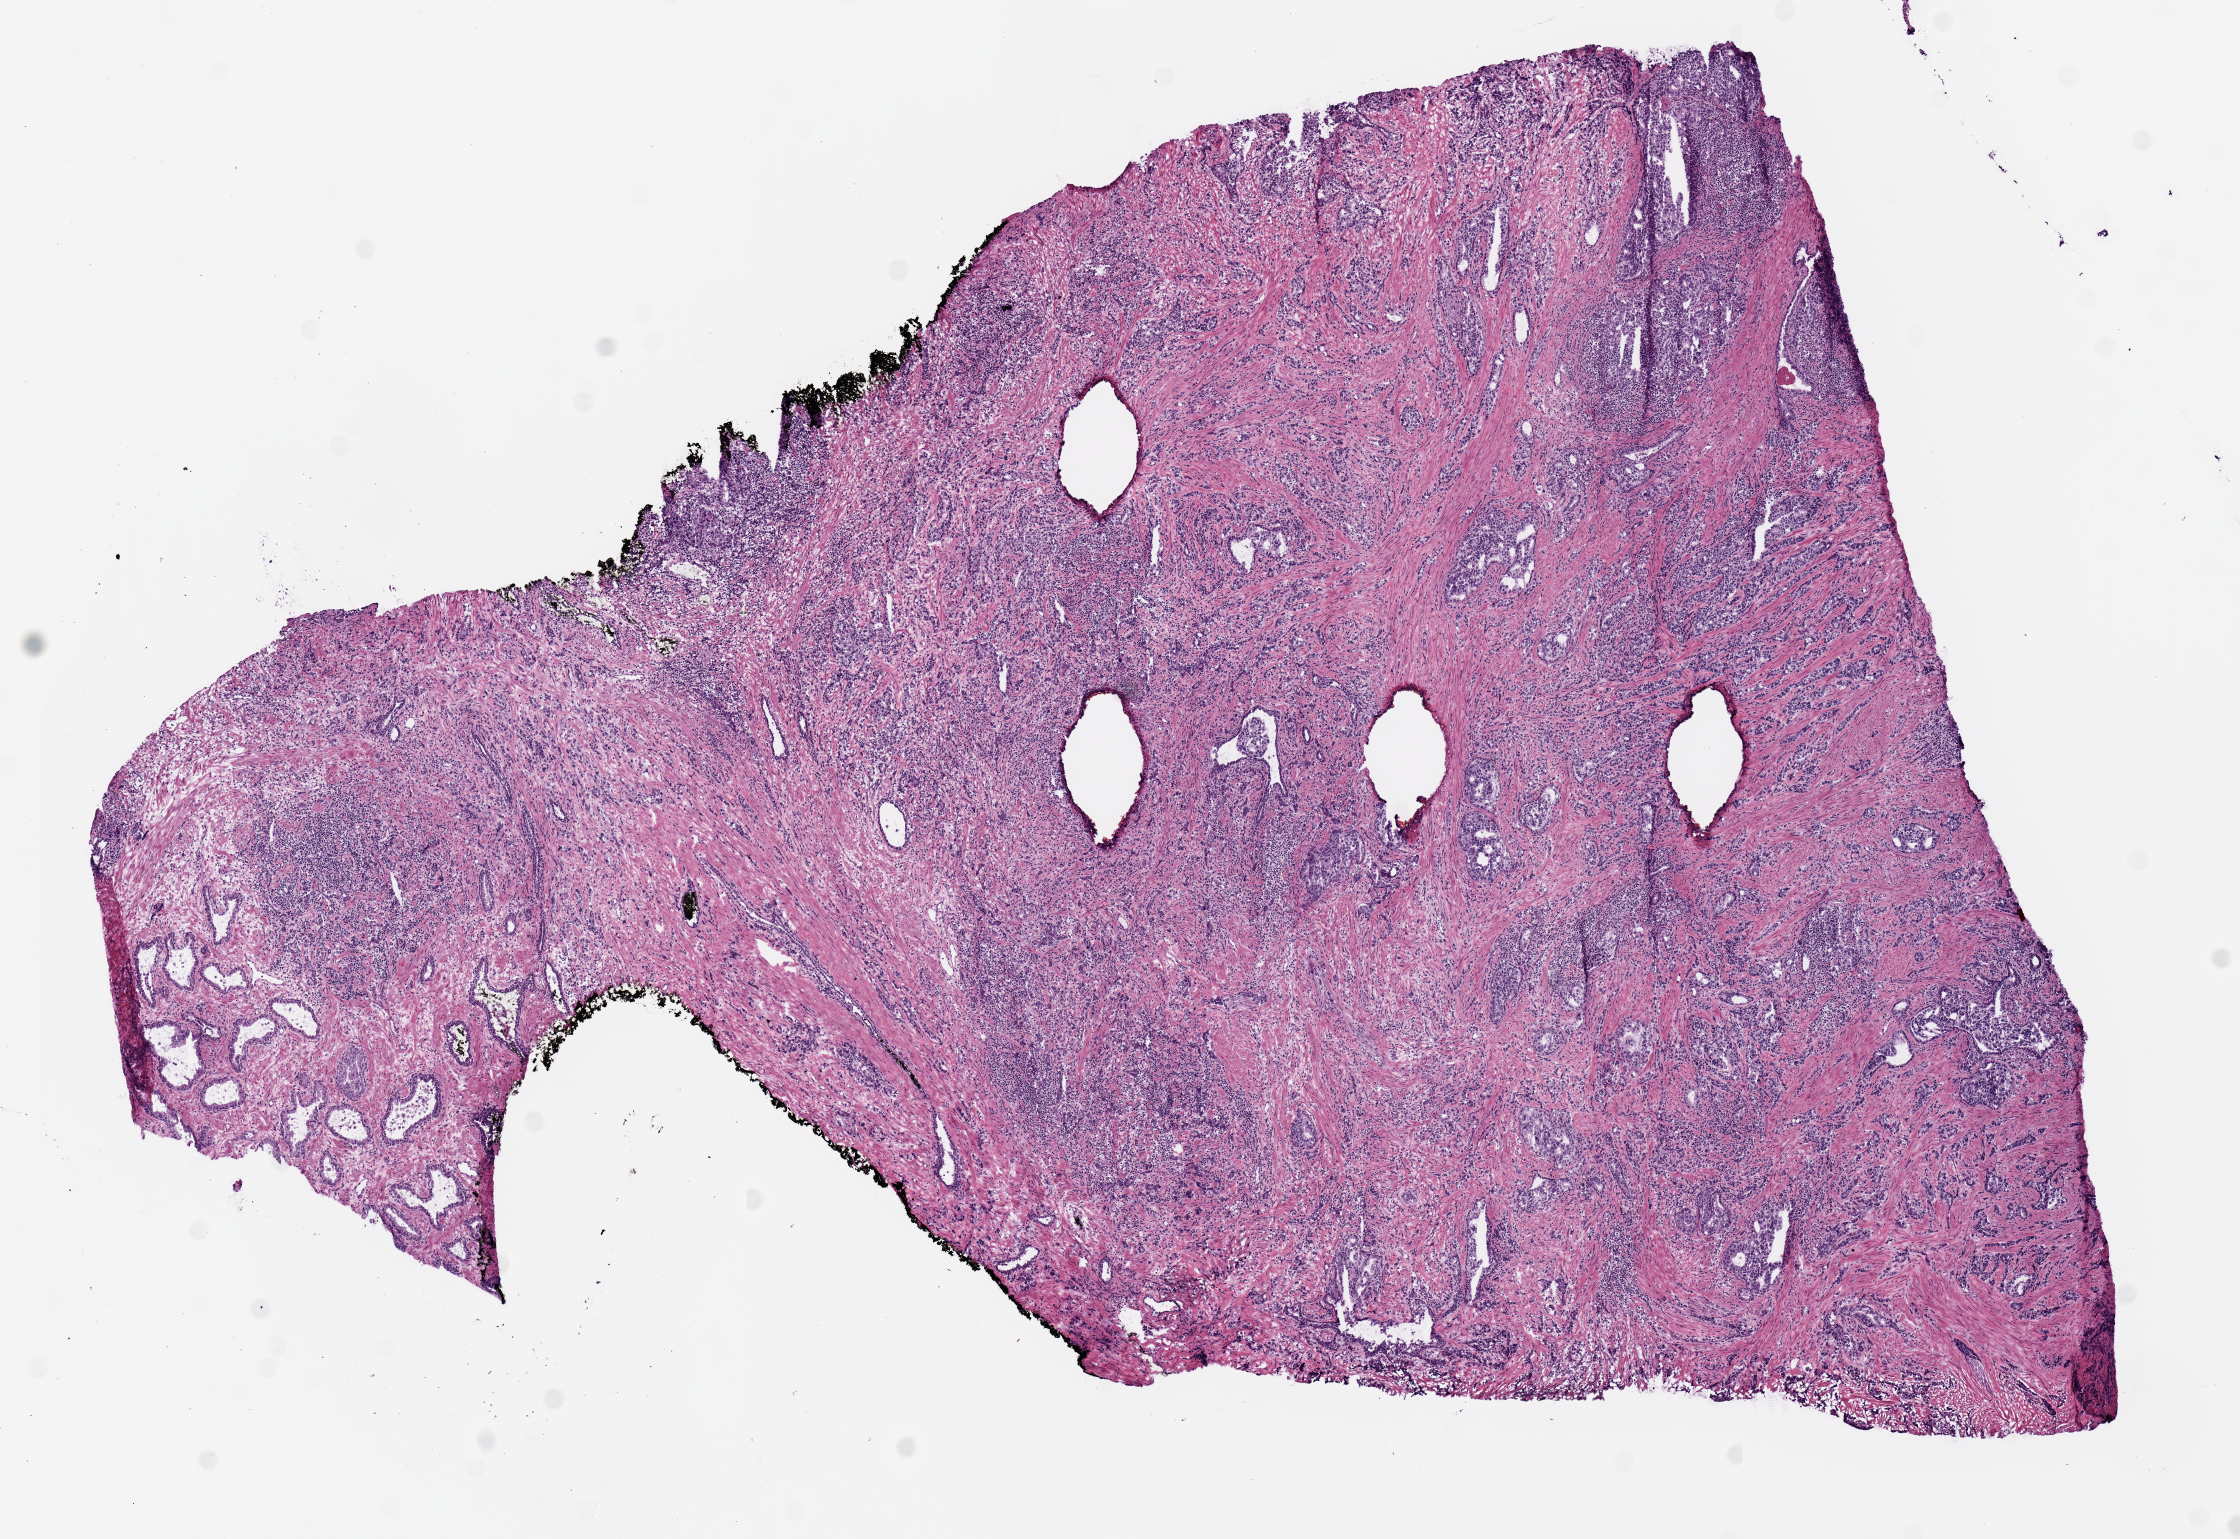
Hematoxylin and eosin (H&E) stained whole-slide image, low-resolution overview of the scanned area, about 8.9 x 6.1 mm (from a 20x scan); frozen section from the top of the tissue portion; sample: primary tumour, prostate. Male patient; age at initial diagnosis 55 years. Gleason score: 8 (4+4). Pathologist review of this section (percent, as recorded): tumour cells 0%, tumour nuclei 70%, normal cells 0%, stromal cells 0%, necrosis 0%.
Lymph nodes positive (case pathology): 0 of 5 examined. Pathologic diagnosis: Acinar cell carcinoma.